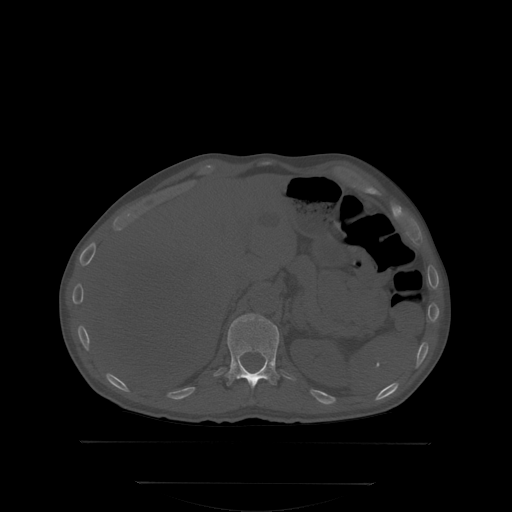
CT including the spine, one axial slice. Position 168 of 350 along the scan axis. Bone window (W 1800 / L 400 HU). 512 × 512 image matrix. Male patient, age 58 years. From the clinical record (not read from this slice): primary cancer: prostate; vertebrae with lytic lesions (as recorded): L1.
Outlined on this slice (semi-automatically segmented with operator editing):
- T12 vertebra: bounding box <226,314,280,388> (left, top, right, bottom; pixels)